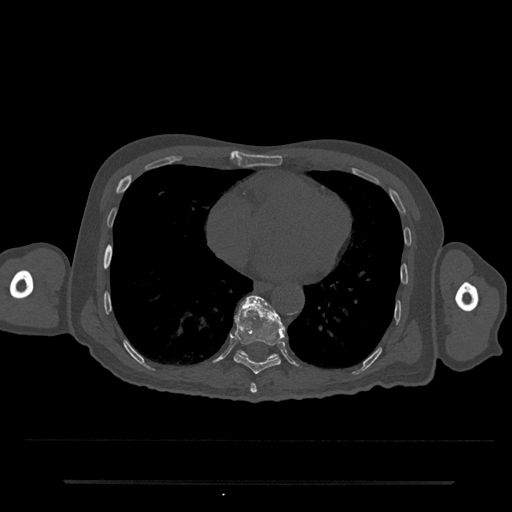
CT including the spine, one axial slice; slice 356 of 797 in the series (ordered by position); 120 kVp; bone window (W 1800 / L 400 HU); 0.5 mm slice thickness; 512 × 512 image matrix, field of view 427 × 427 mm. Patient: male, 74 years. From the clinical record (not read from this slice): primary cancer: prostate.
Outlined on this slice (semi-automatically segmented with operator editing):
- T10 vertebra: bounding box (x1, y1, x2, y2) in pixels: (238, 296, 277, 360)
- T8 vertebra: (250, 383, 257, 394)
- T9 vertebra: (233, 296, 285, 374)